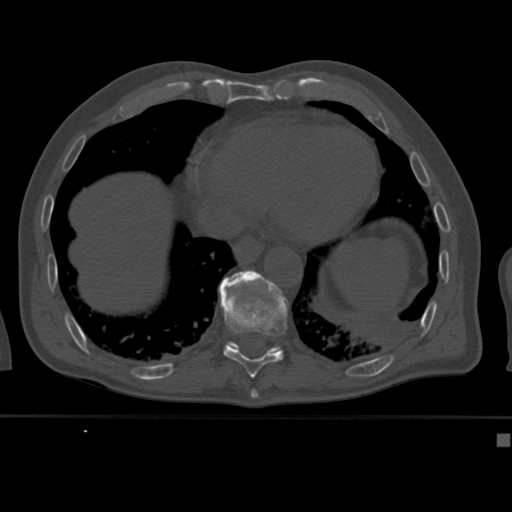
CT including the spine, one axial slice; position 225 of 430 along the scan axis; bone window (W 1800 / L 400 HU); 1.5 mm slice thickness; 512 × 512 image matrix, field of view 337 × 337 mm. Male patient, age 64 years. Case-level facts recorded for this patient, not image findings: primary cancer: uterus.
Annotated regions visible in this slice (semi-automatically segmented with operator editing):
- T10 vertebra: bounding box [x1, y1, x2, y2] px = [219, 273, 289, 378]
- T11 vertebra: [220, 270, 280, 352]